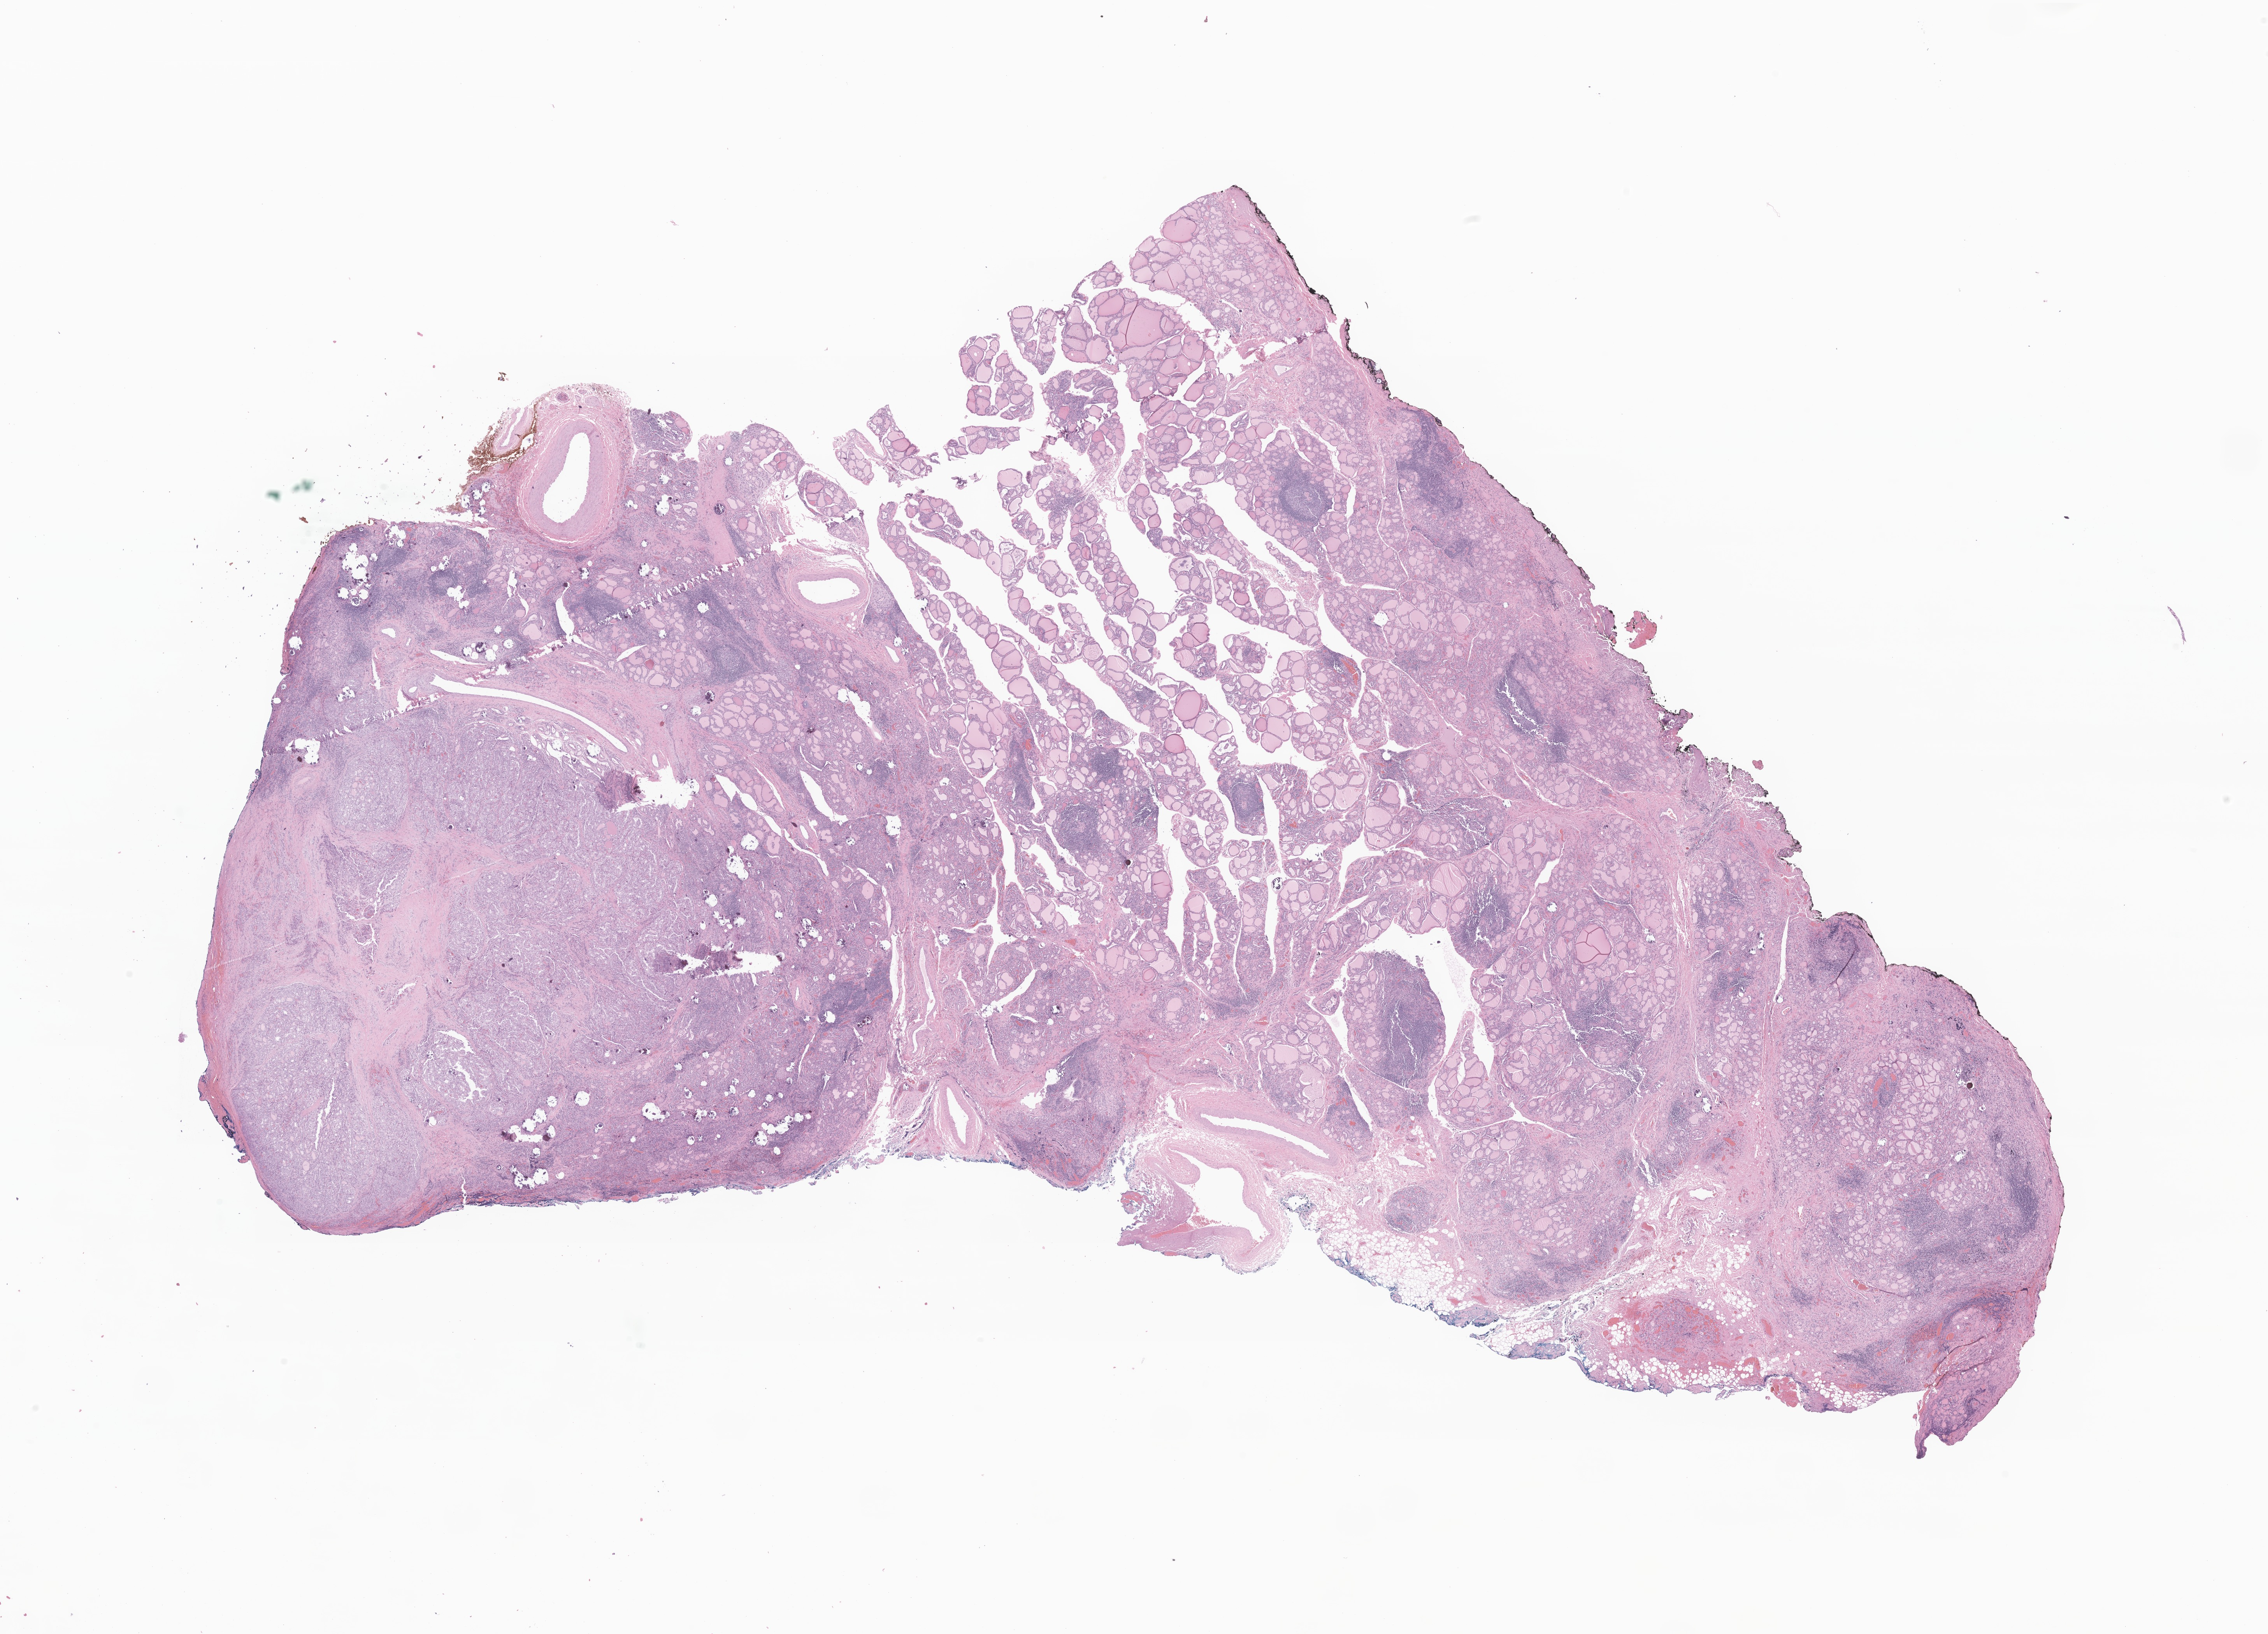
Haematoxylin and eosin whole-slide image of tumor tissue from the thyroid — low-resolution overview of the scanned area, about 24.6 x 17.7 mm. Formalin-fixed paraffin-embedded section. Female patient, age 215 months (17 years 11 months).
Diagnosis (ICD-O-3 morphology term): Papillary carcinoma, NOS.